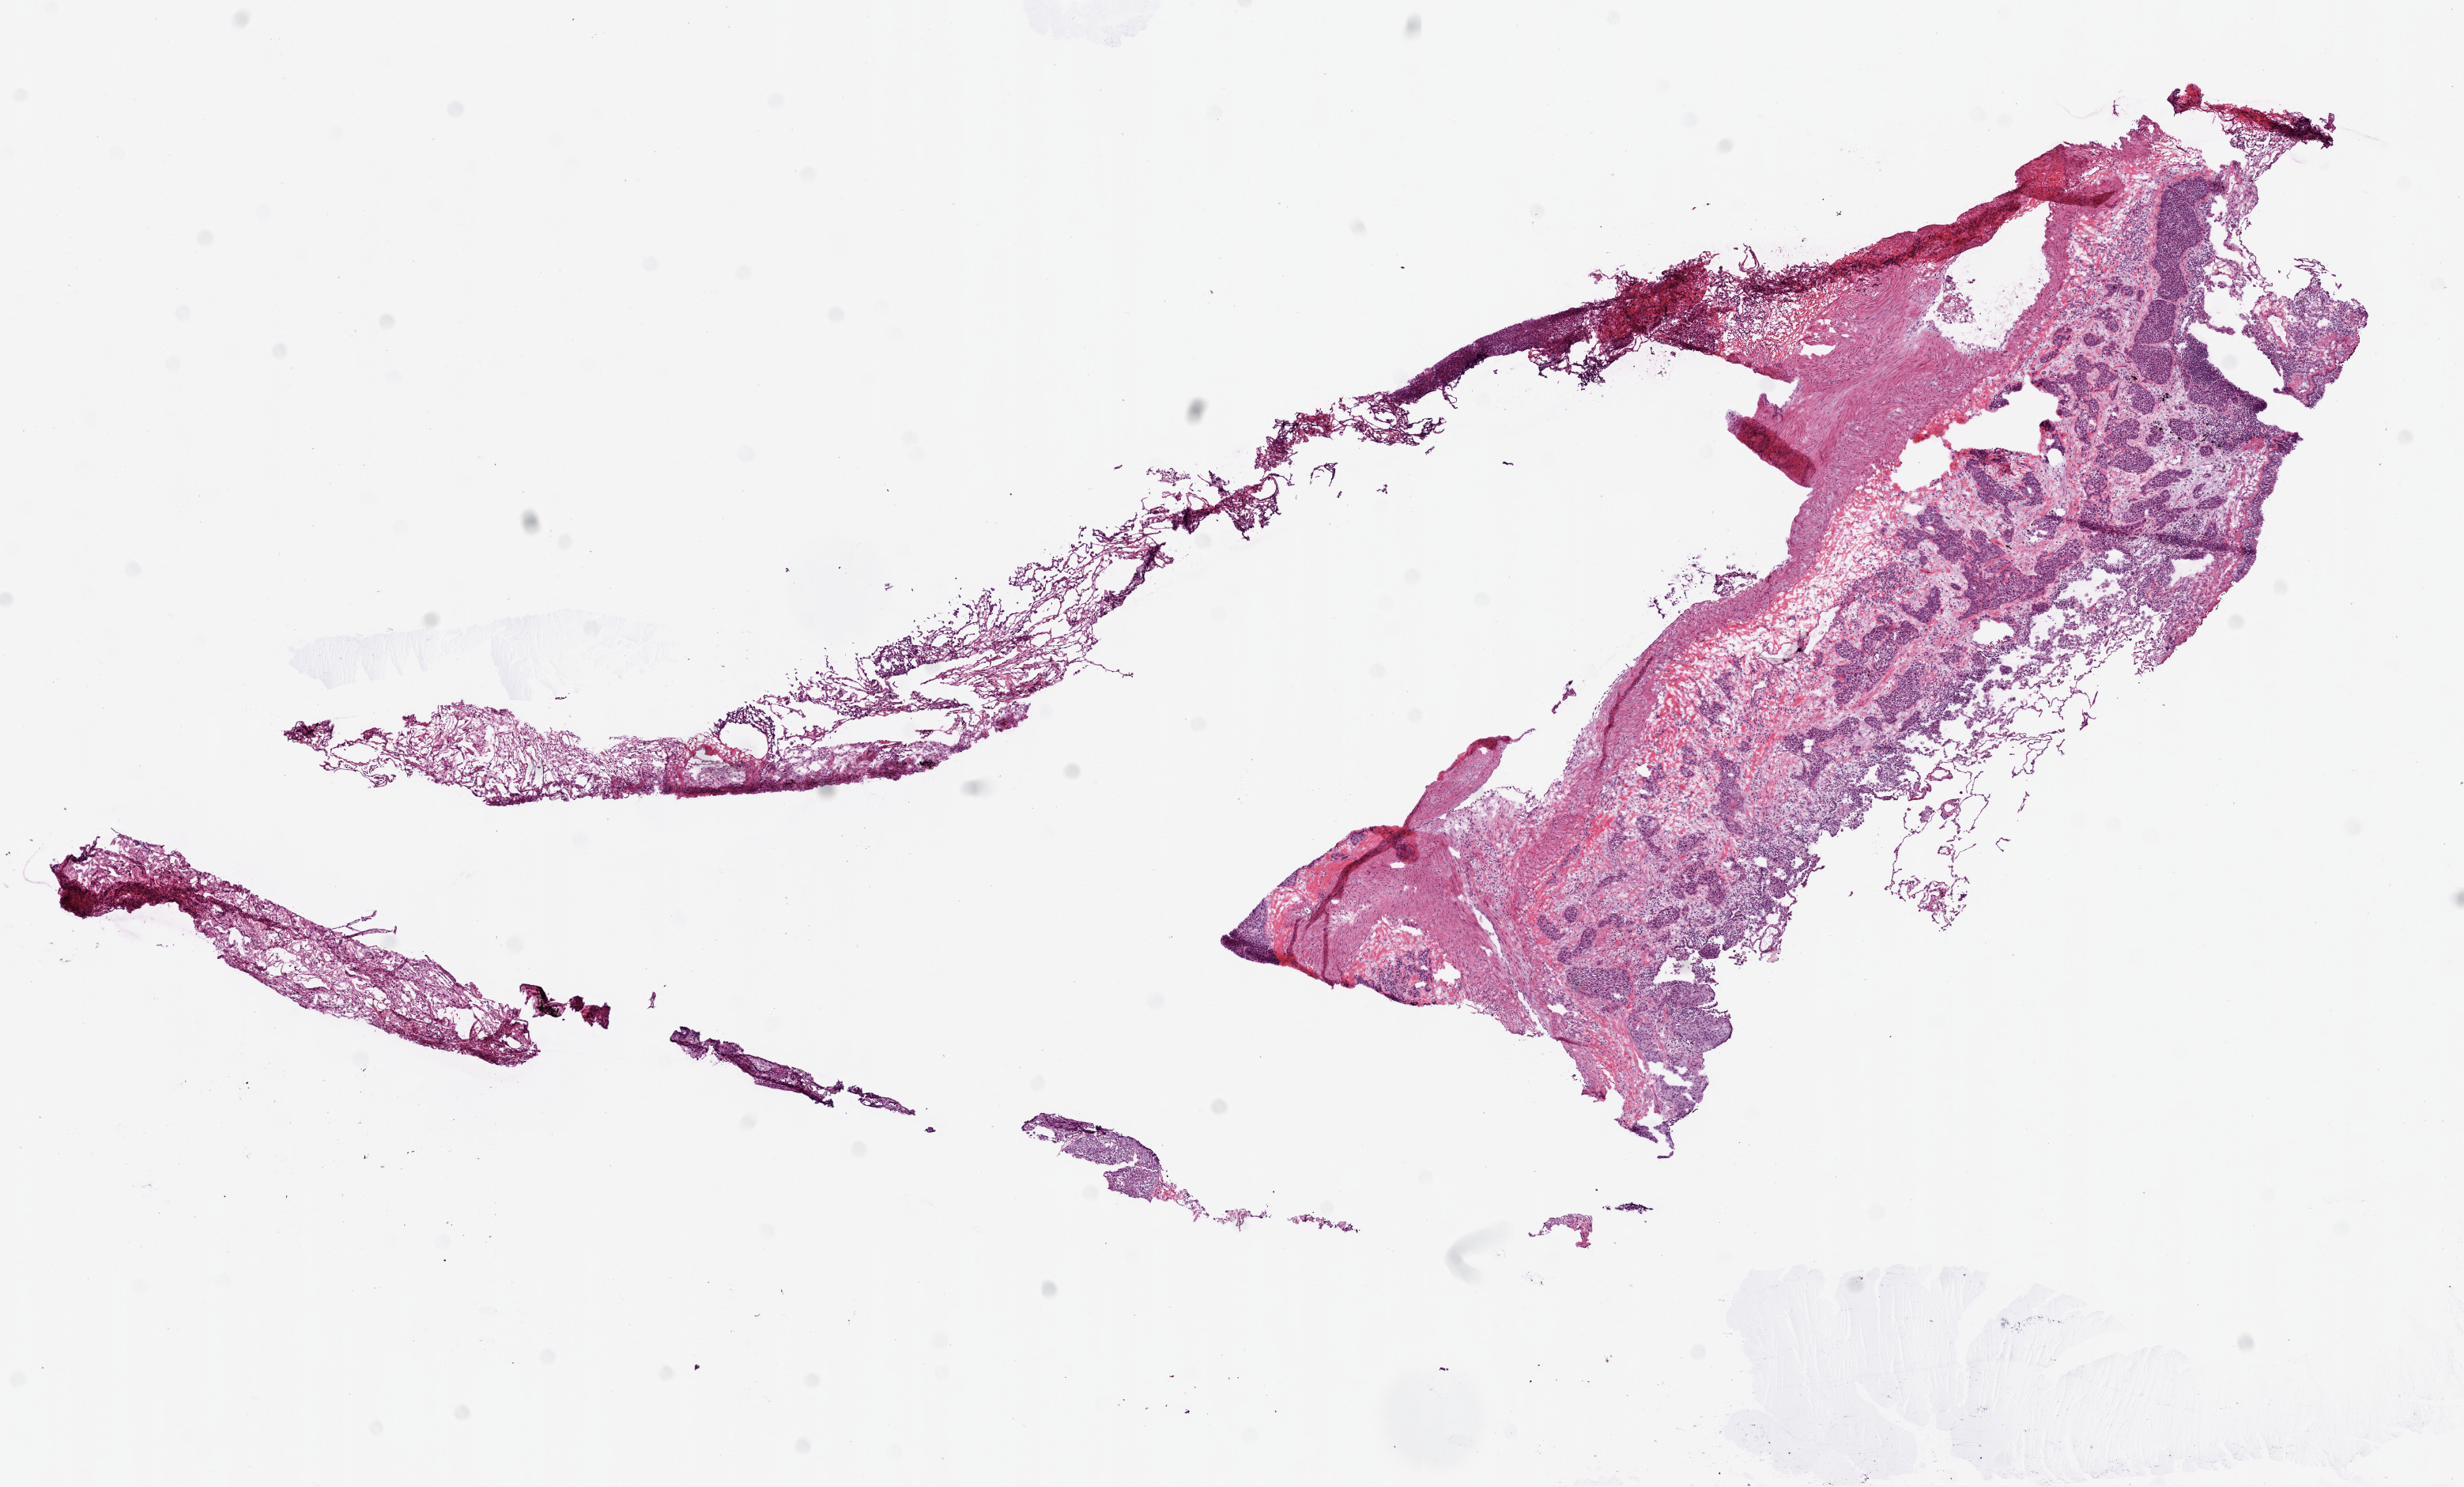
Digitized H&E-stained tissue section (whole slide), low-resolution overview of the scanned area, about 12.6 x 7.6 mm (acquisition: 20x scan), frozen section, lung, primary tumour sample. Patient: male, age at initial diagnosis 69 years. Composition of this section per pathologist review: tumour nuclei 60%, necrosis 20%.
- TNM: T1 N0 M0
- pathologic diagnosis: Squamous cell carcinoma, NOS
- AJCC pathologic stage: IA